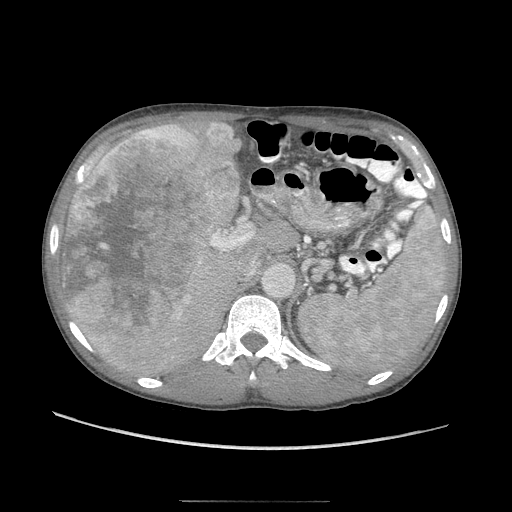
Contrast-enhanced abdominal CT (liver protocol), one axial slice; slice 59 of 103 in the series (ordered by position); 120 kVp; soft-tissue window (W 400 / L 40 HU); 2.5 mm slice thickness; 512 × 512 image matrix, field of view 380 × 380 mm. From the clinical record (not read from this slice): diagnosis: hepatocellular carcinoma (patient treated with transarterial chemoembolisation; whether this scan precedes or follows treatment is not stated here); TNM stage (as recorded): Stage-IIIA; Child-Pugh class: A; tumour differentiation: moderately differentiated; tumour nodularity: multinodular.
Annotated regions visible in this slice (semi-automatically segmented with operator editing):
- liver parenchyma outside the tumour (the mass and vessels are separate outlines, so this box may not span the whole liver): box from (x=54, y=118) to (x=274, y=376) px
- mass: (x=61, y=121)–(x=242, y=364)
- liver vessels: (x=92, y=218)–(x=223, y=352)